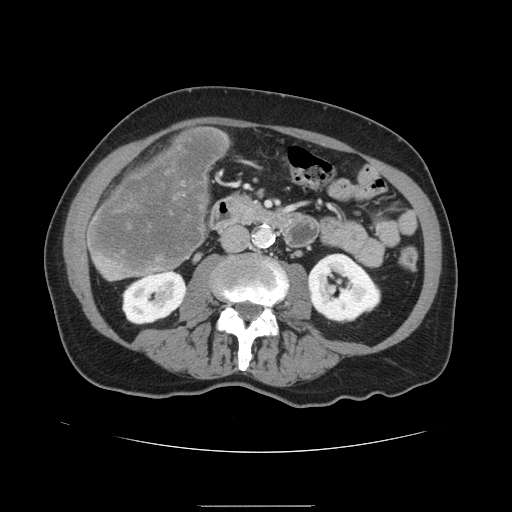
Contrast-enhanced abdominal CT, one axial slice. 120 kVp. Intravenous contrast given. Soft-tissue window (W 400 / L 40 HU). 2.5 mm slice thickness. 512 × 512 image matrix, field of view 386 × 386 mm. Male patient, age 74 years. From the clinical record (not read from this slice): diagnosis: colorectal cancer liver metastases, imaged before liver resection; multiple liver metastases: no; largest metastasis: 14.5 cm; disease in both lobes: yes.
Annotated regions visible in this slice (outlined manually by an expert reader):
- liver: bounding box (x1, y1, x2, y2) in pixels: (87, 127, 229, 281)
- liver metastasis: (90, 131, 227, 272)